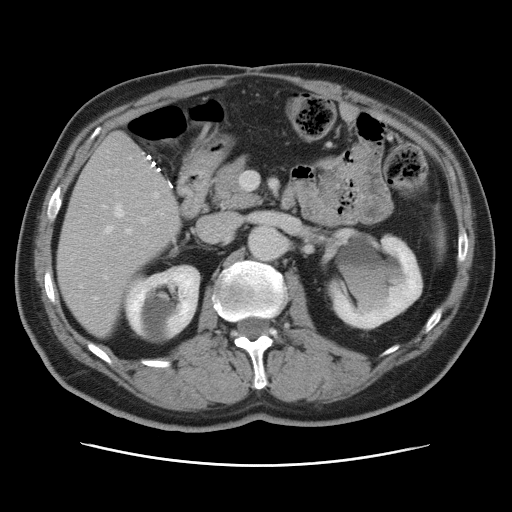
Contrast-enhanced abdominal CT, one axial slice; position 36 of 80 along the scan axis; intravenous contrast given; soft-tissue window (W 400 / L 40 HU); 5 mm slice thickness; 512 × 512 image matrix. Male patient, age 69 years. Case-level facts recorded for this patient, not image findings: diagnosis: colorectal cancer liver metastases, imaged before liver resection; multiple liver metastases: no; largest metastasis: 5 cm; chemotherapy before resection: no.
Structures marked on this image (expert manual segmentation):
- hepatic veins: bounding box (x1, y1, x2, y2) in pixels: (80, 206, 144, 287)
- liver: (58, 133, 181, 336)
- planned liver remnant (the part of the liver to remain after resection): (58, 195, 181, 336)
- portal vein (with intrahepatic branches): (101, 228, 132, 279)